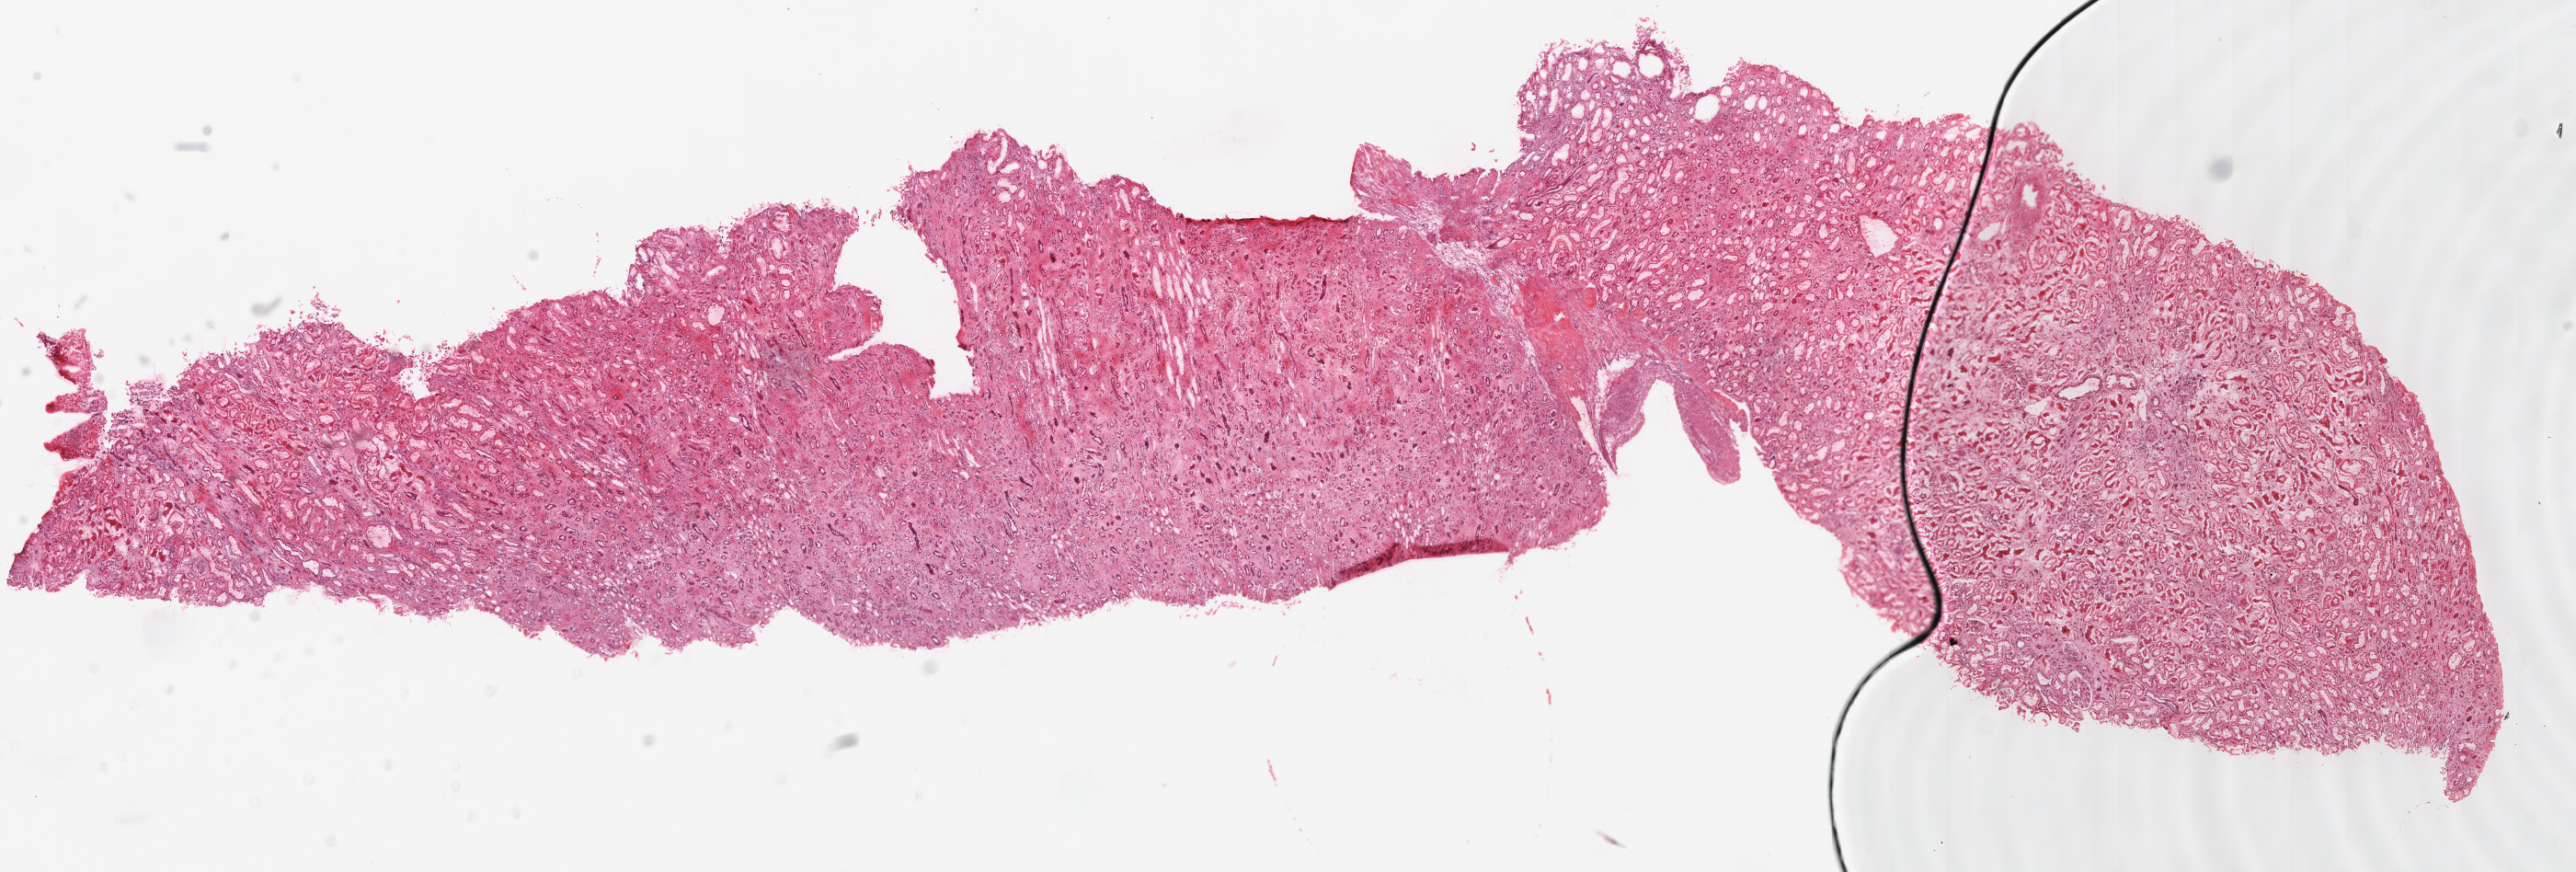
Whole-slide histology image, H&E — shown as a low-resolution overview of the whole scanned area (about 22.0 x 7.5 mm). Frozen section from the top of the tissue portion. Solid tissue normal (non-tumour tissue) sample from the kidney. Male patient; age at initial diagnosis 71 years. Infiltration values recorded for this section: lymphocyte infiltration 0%, monocyte infiltration 0%, neutrophil infiltration 0%.
This section: solid tissue normal sample (biorepository sample class). Patient diagnosis: Renal cell carcinoma, chromophobe type.